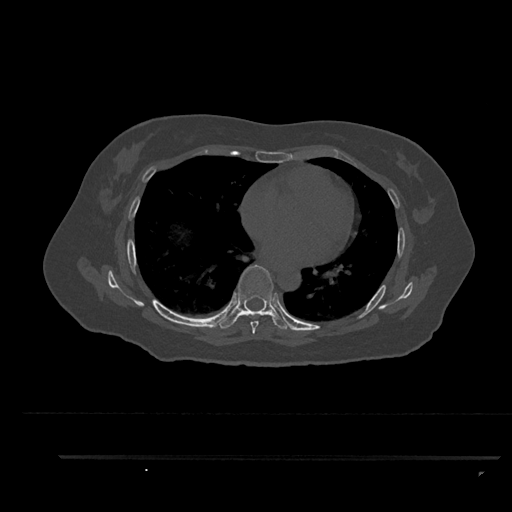
CT including the spine, one axial slice; position 526 of 797 along the scan axis; reconstruction kernel Br40s/3; bone window (W 1800 / L 400 HU); 512 × 512 image matrix, field of view 408 × 408 mm. Female patient, age 44 years. Case-level facts recorded for this patient, not image findings: primary cancer: renal.
Annotated regions visible in this slice (semi-automatic segmentation, software-assisted and operator-edited):
- T6 vertebra: bounding box <250,314,259,334> (left, top, right, bottom; pixels)
- T7 vertebra: <218,265,290,329>